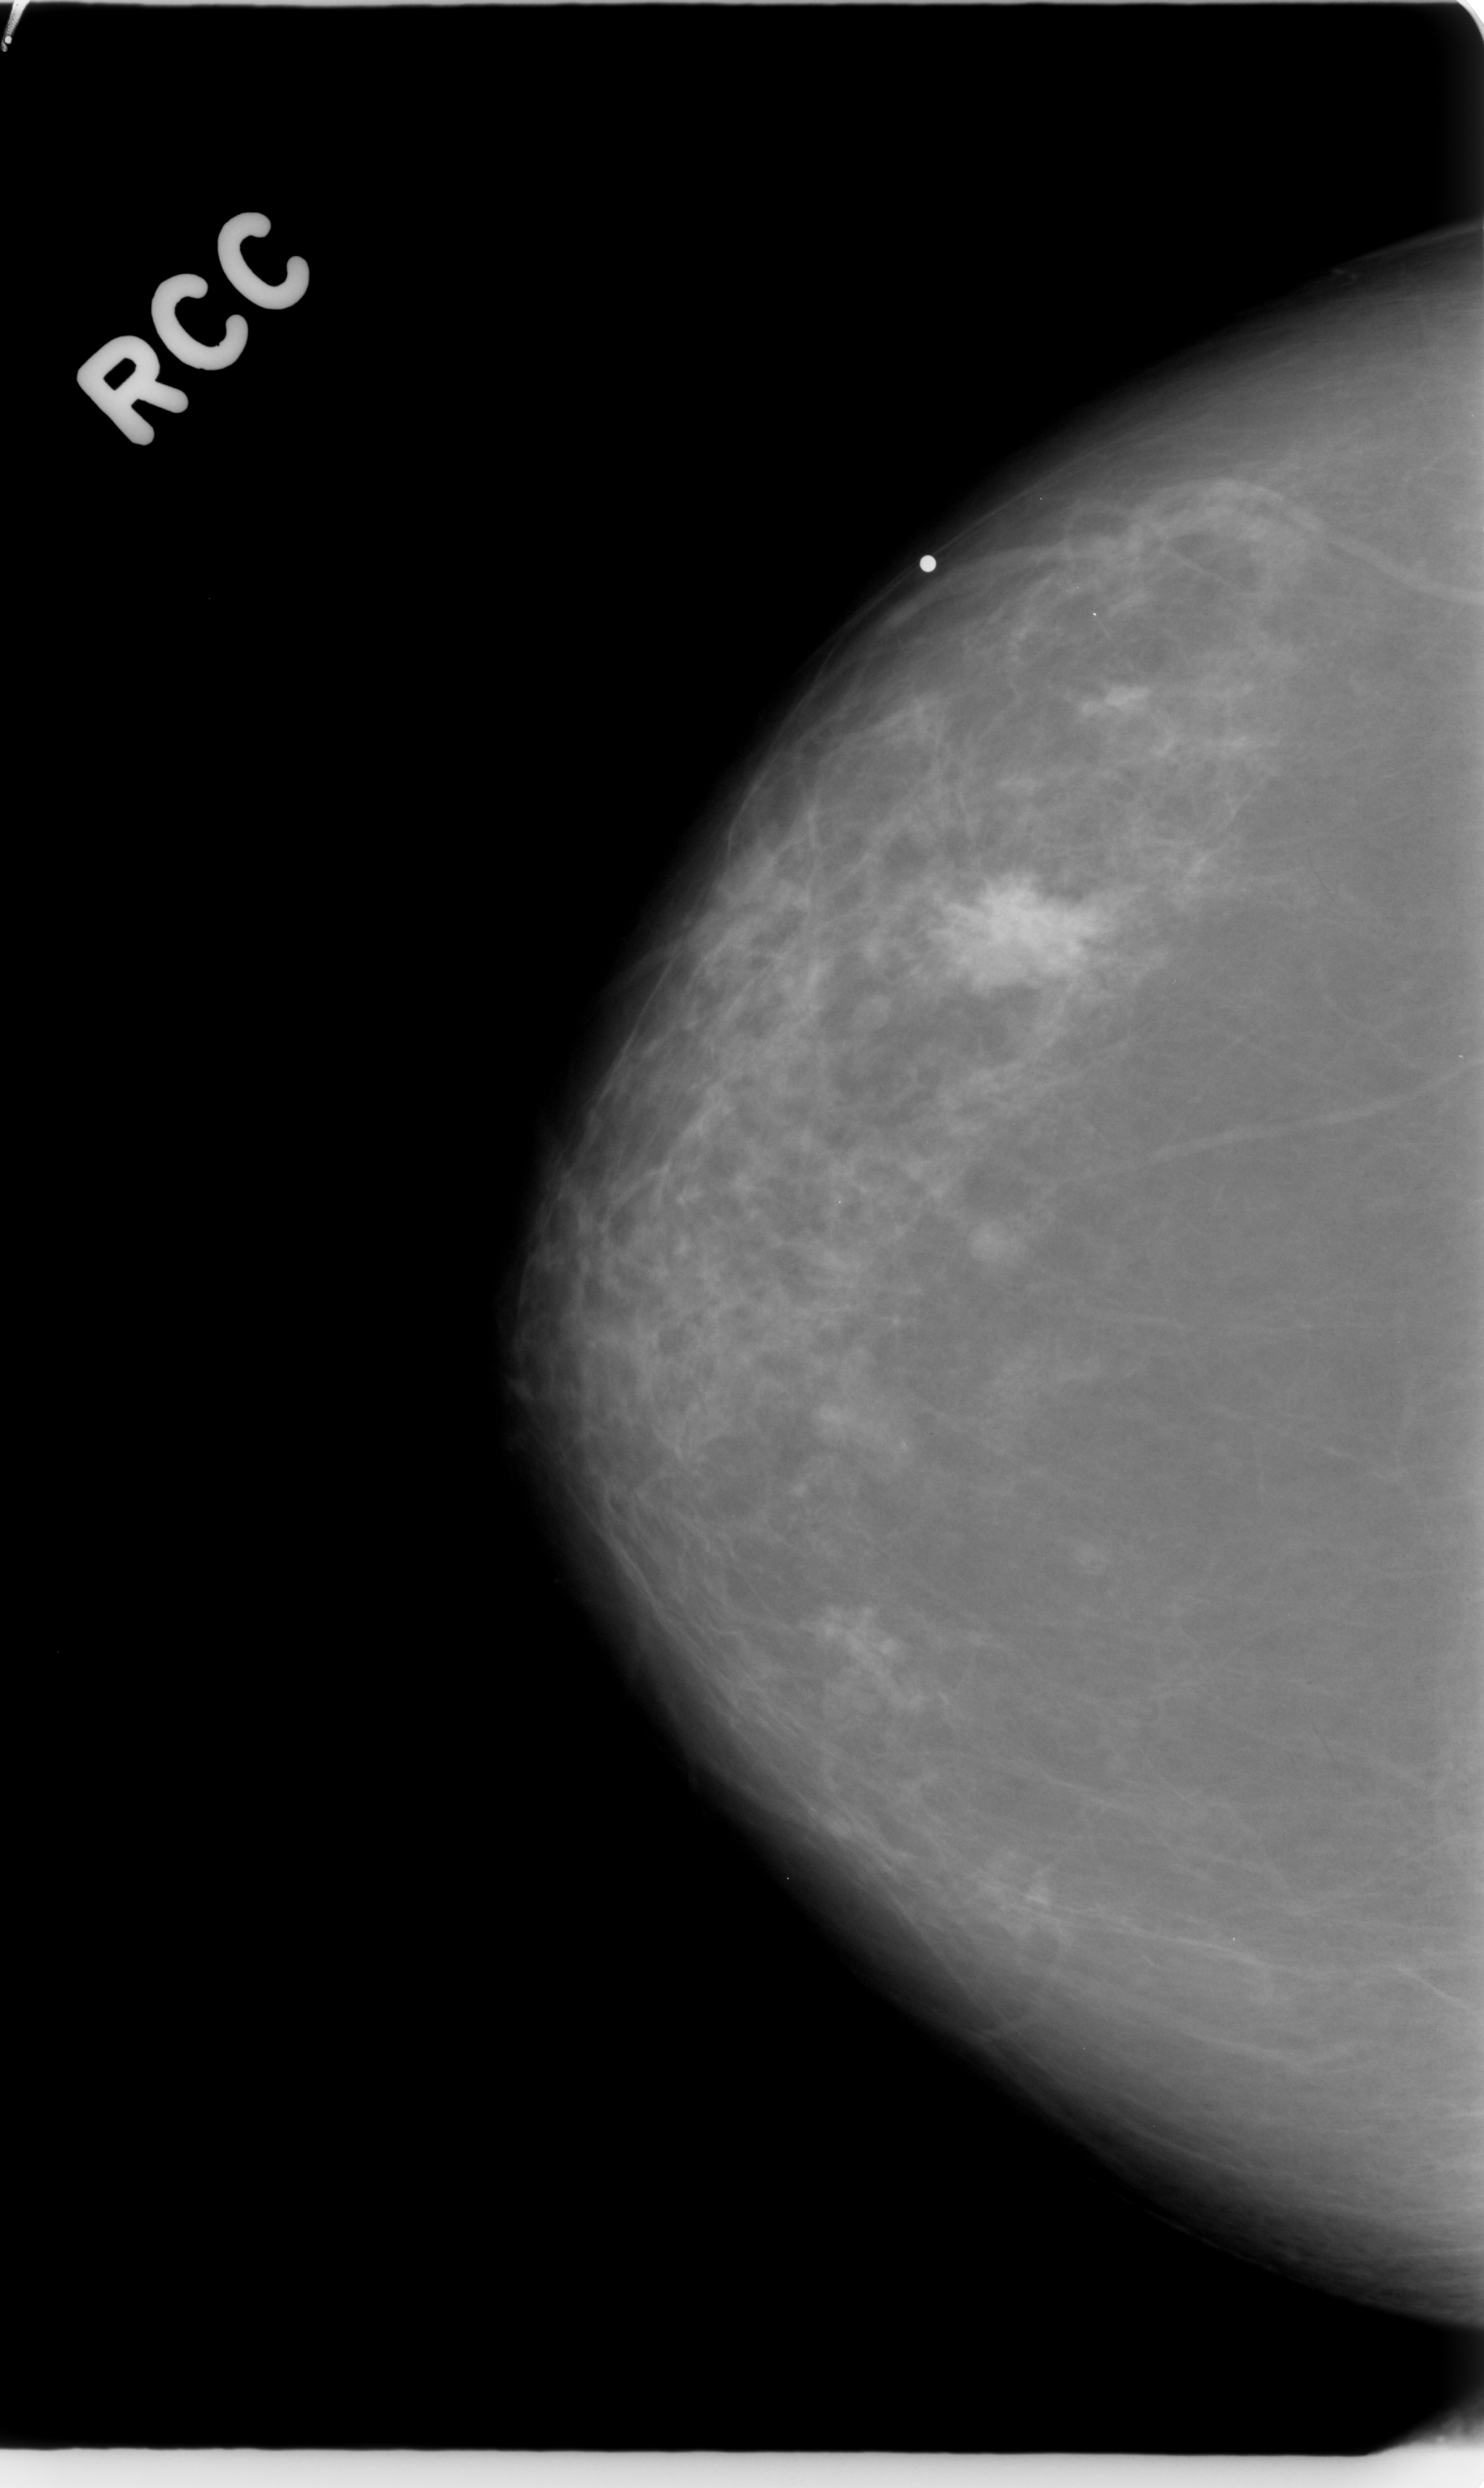
Mammogram (digitized film). Right breast. Craniocaudal (CC) view. Breast composition: almost entirely fatty (BI-RADS density category 1 of 4). 1484 × 2488 image matrix.
Marked abnormalities (boxes around the expert regions of interest):
- mass, shape irregular, margins spiculated; BI-RADS assessment category 5; pathology (as recorded): malignant: bounding box (x1, y1, x2, y2) in pixels: (927, 862, 1118, 999)